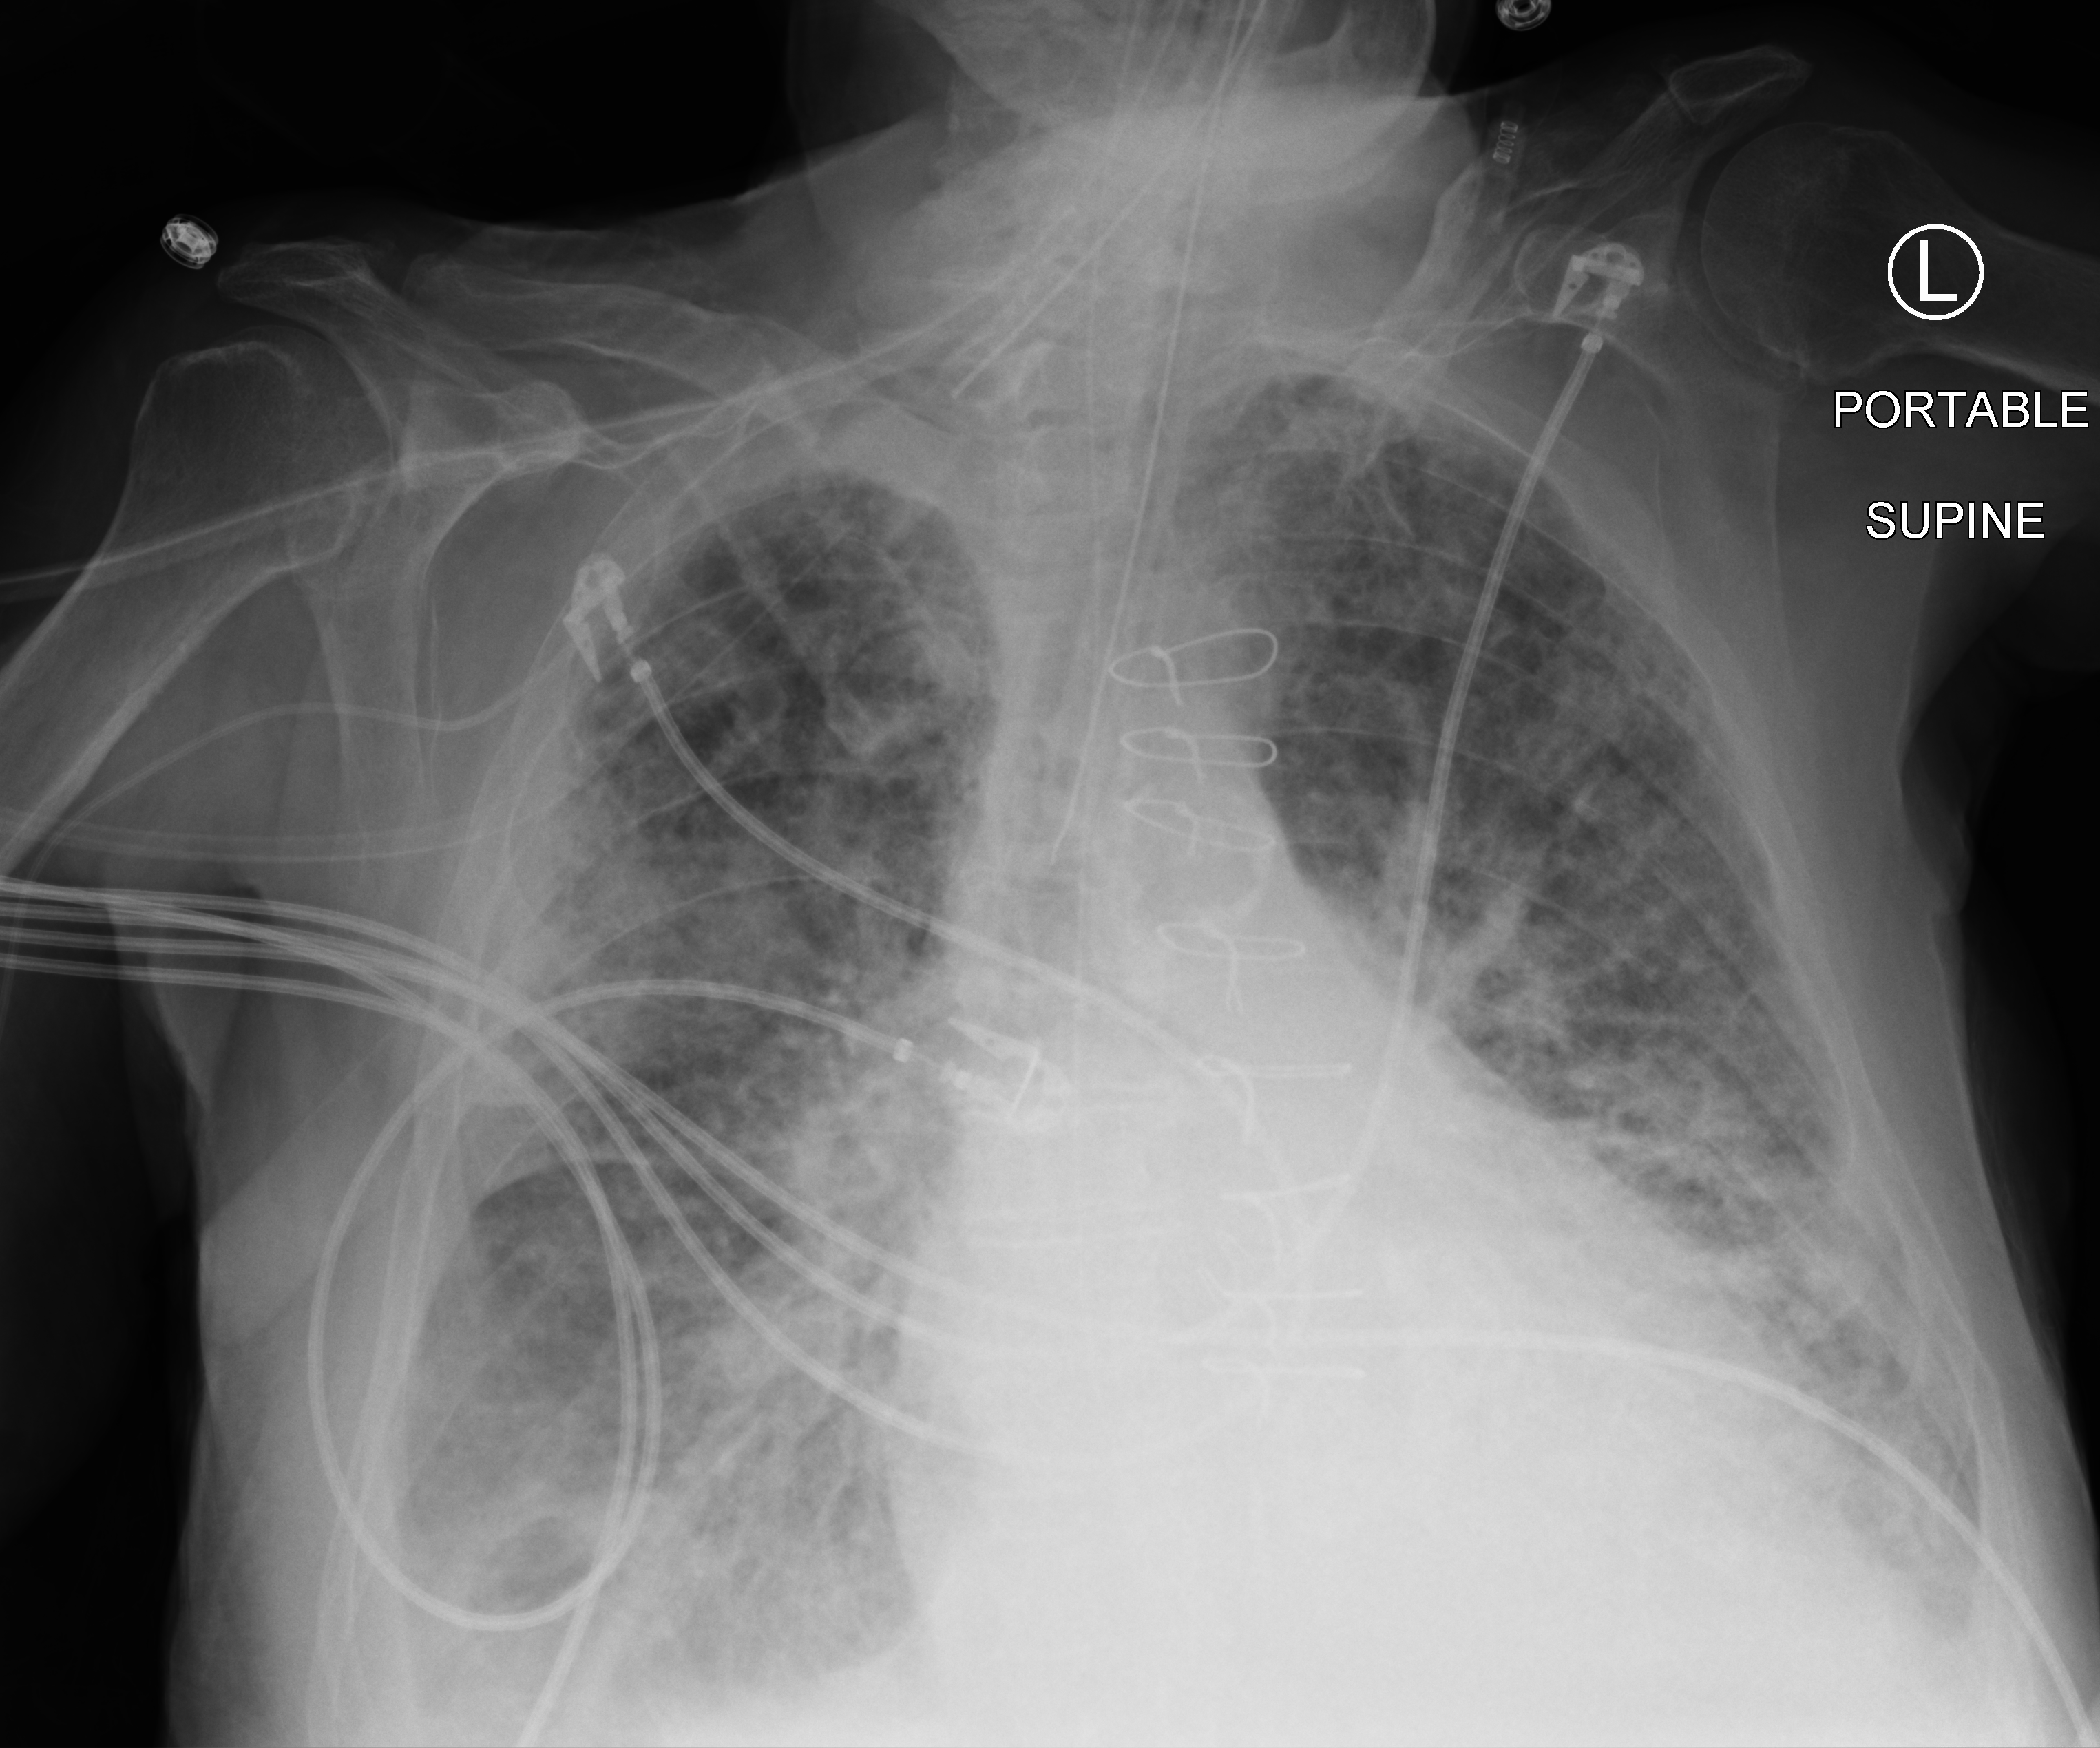
Bedside chest radiograph (computed radiography), anteroposterior (AP) projection. Patient hospitalised with COVID-19; male, aged 75–90 years.
From the hospital-stay record, not from the radiograph (when in the stay this image was taken is not recorded):
- mechanically ventilated during this hospital stay: yes
- admitted to intensive care during this hospital stay: yes